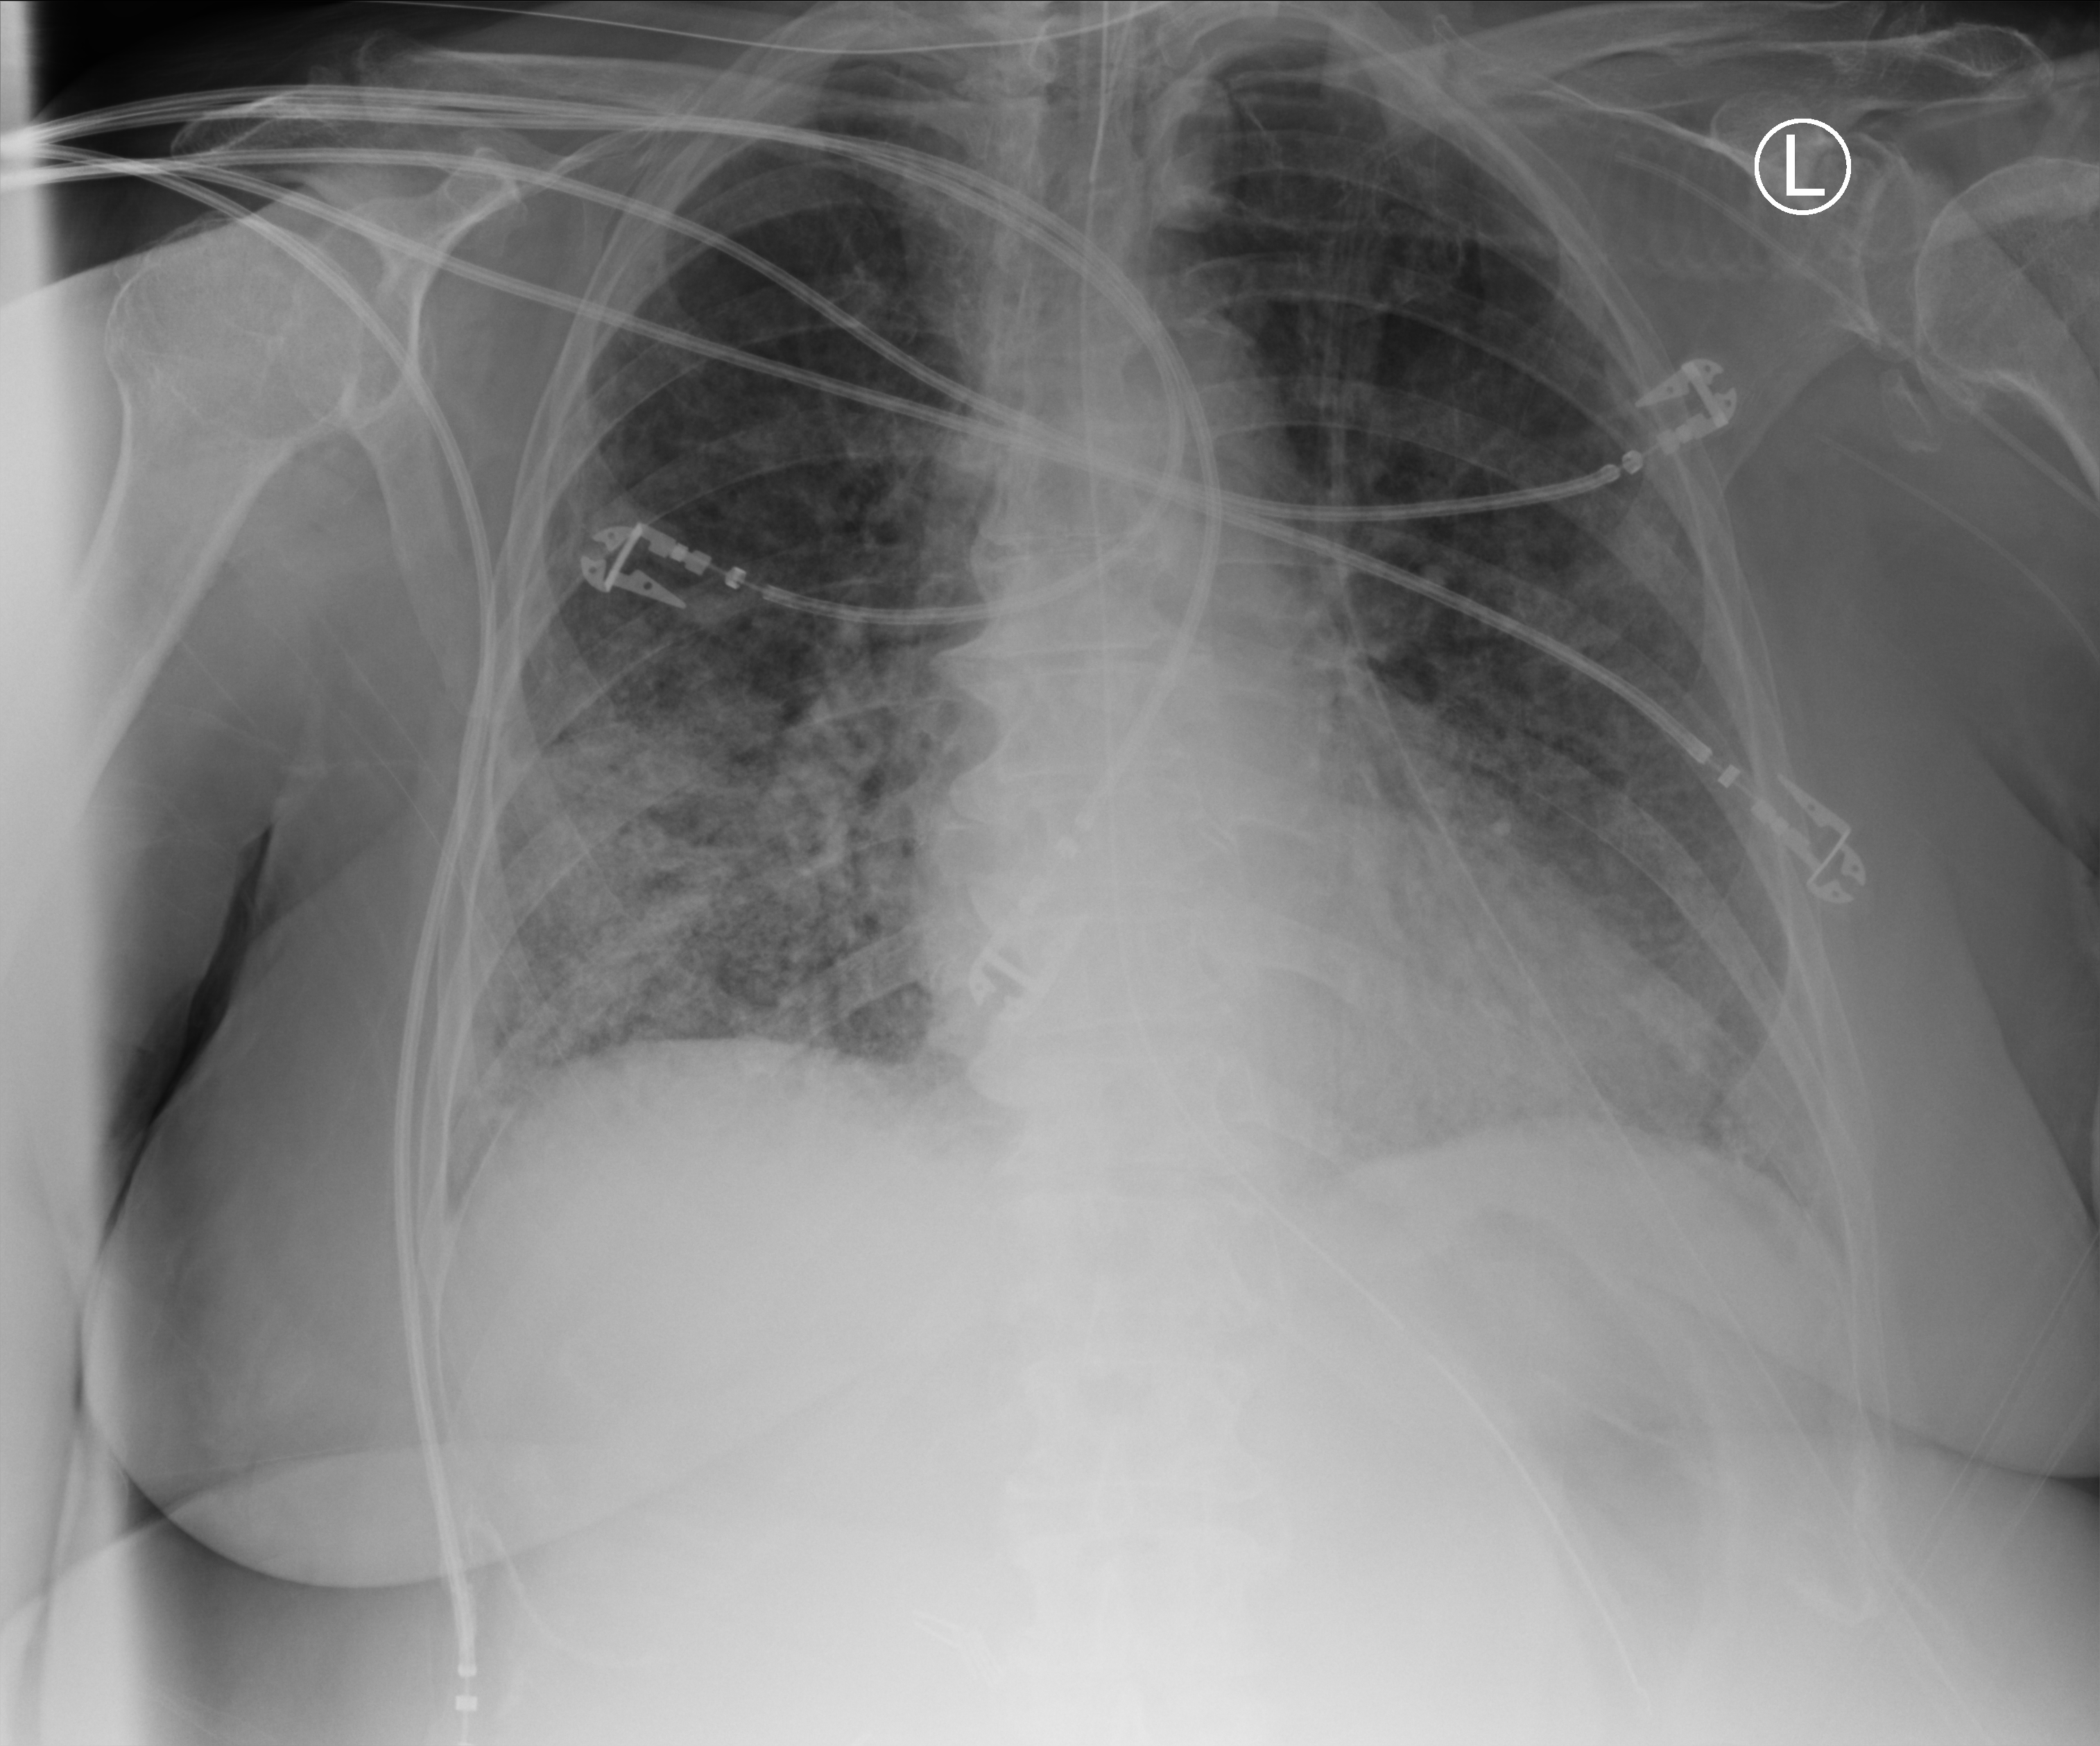
Bedside chest radiograph (computed radiography); anteroposterior (AP) projection. Patient hospitalised with COVID-19; female, aged 75–90 years.
Hospital-stay facts (about this admission, not read from this image; timing relative to this image not recorded): admitted to intensive care during this hospital stay: no; other chronic lung disease (admission record): no; diabetes (admission record): no.